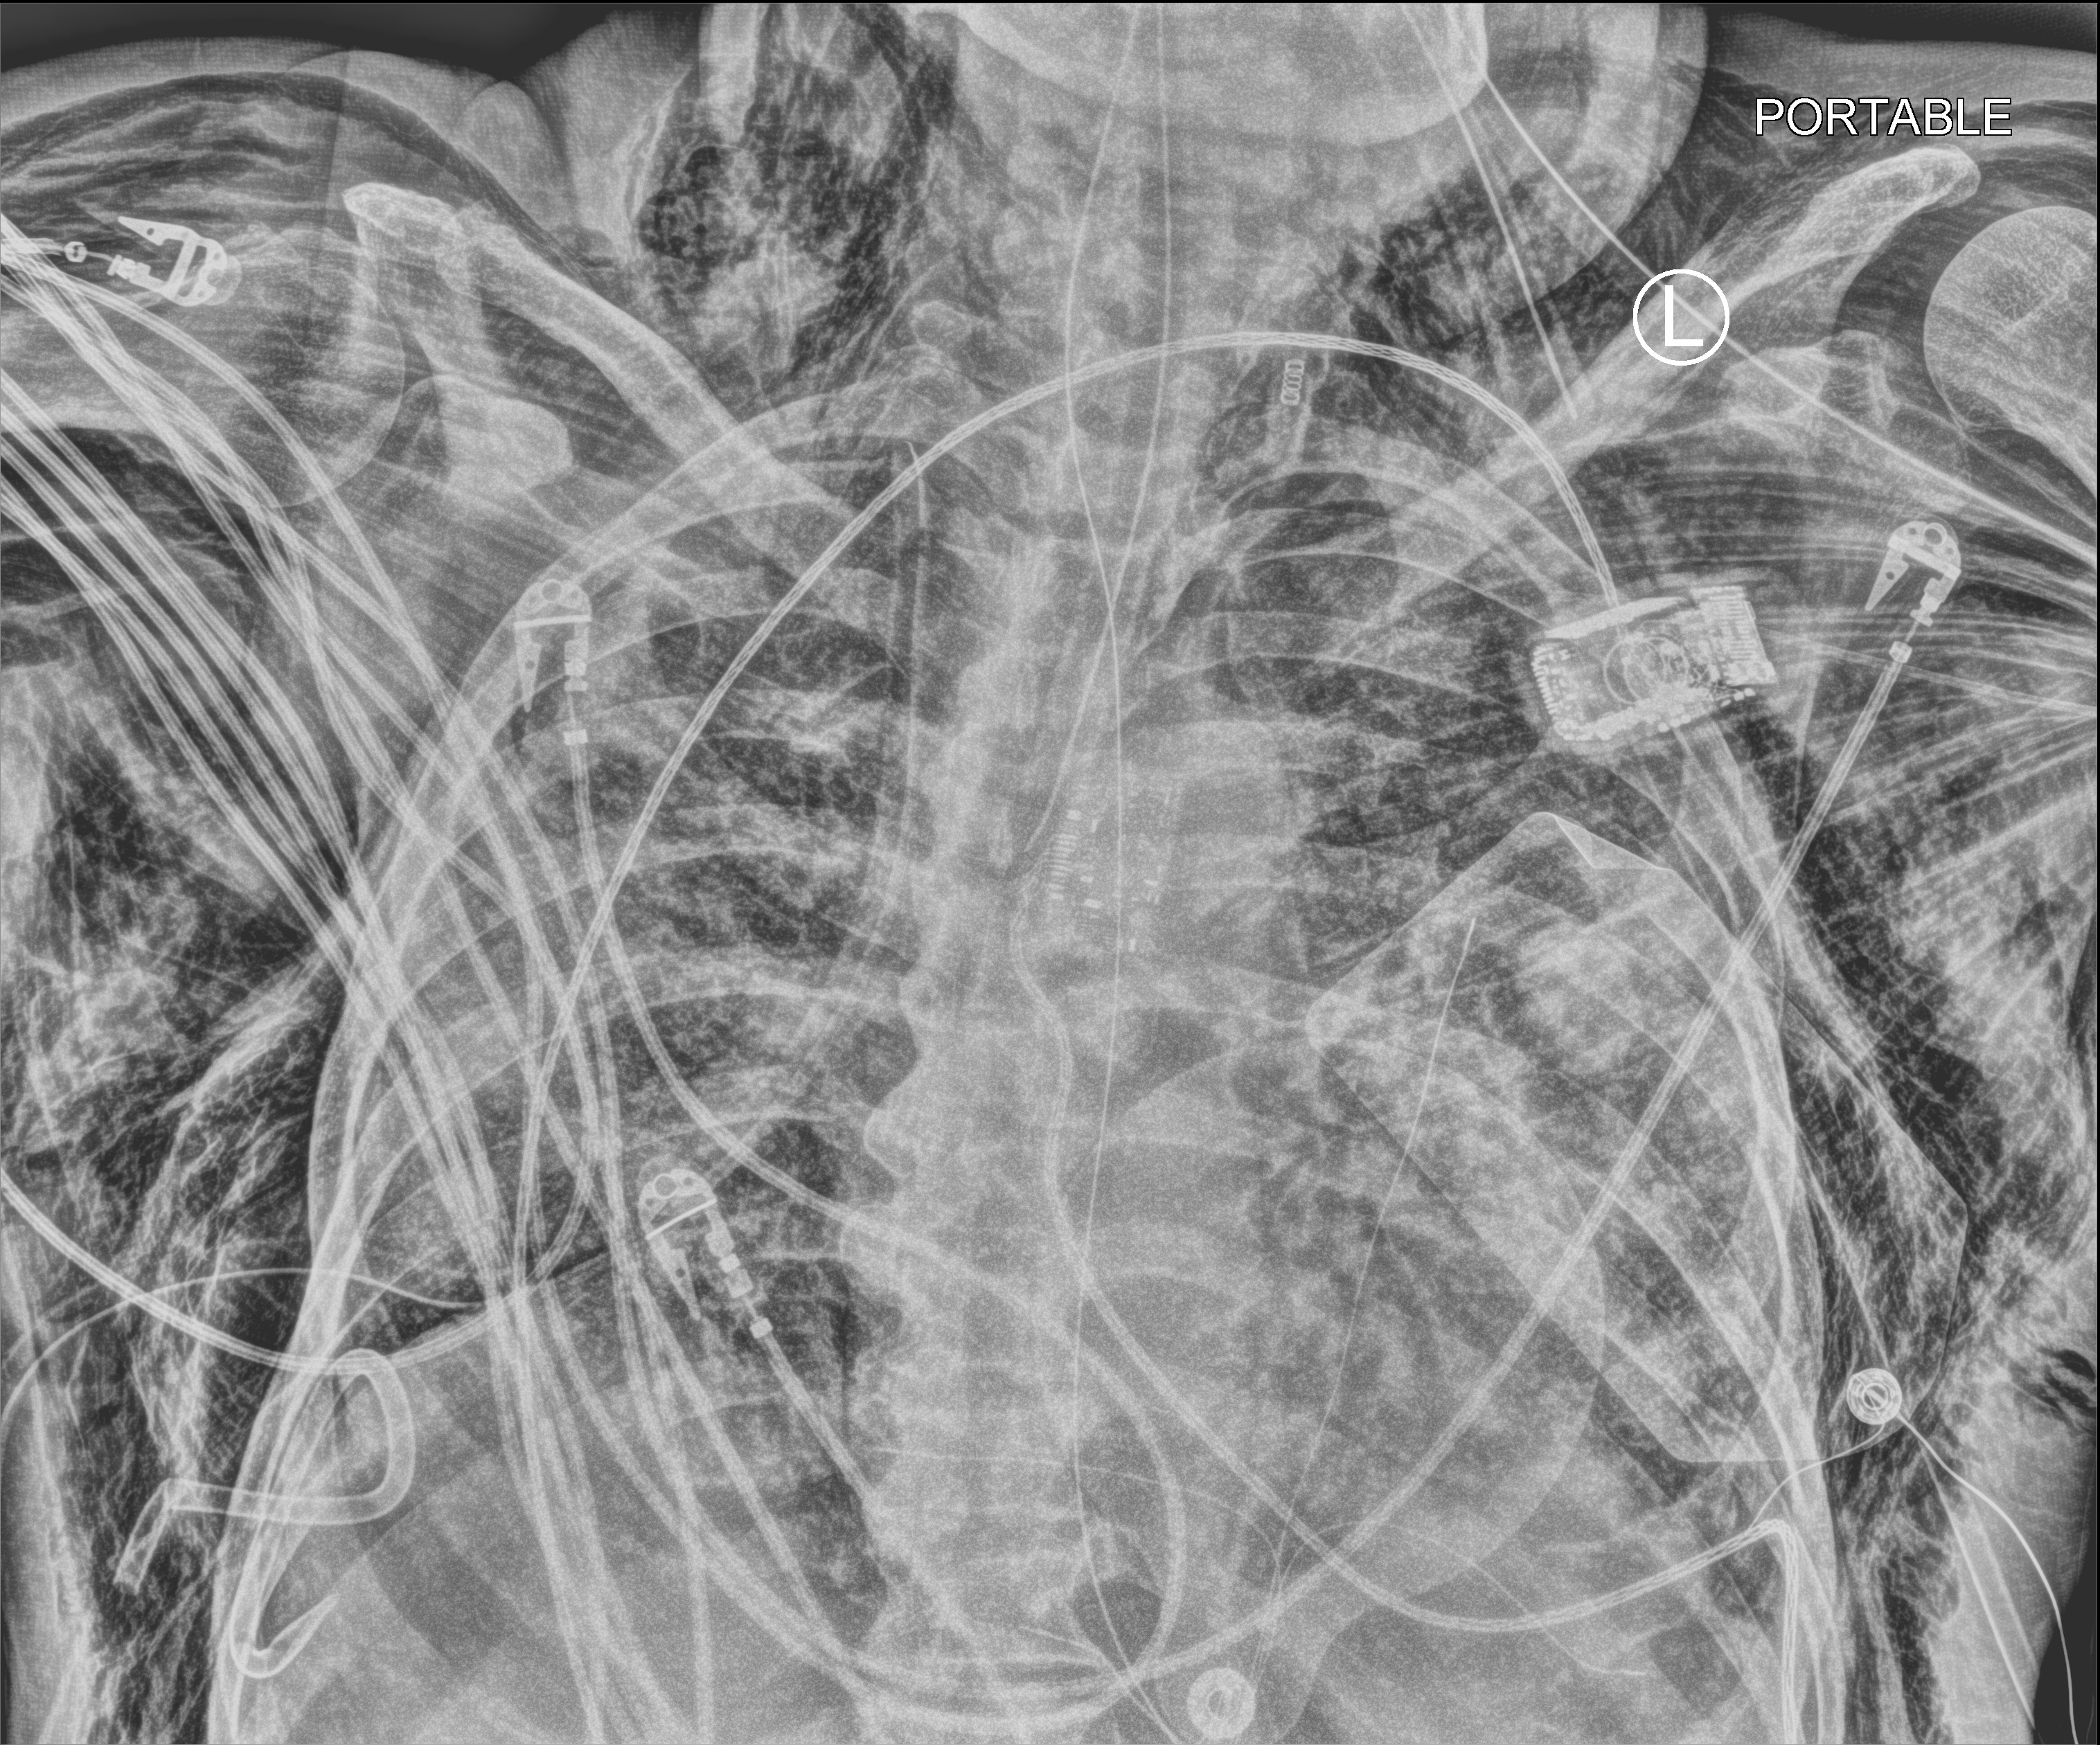
Portable chest radiograph; anteroposterior (AP) projection. Patient hospitalised with COVID-19; male, aged 75–90 years.
Admission-level facts for this patient (not findings on this image; timing relative to this image not recorded): chronic kidney disease (admission record): no.